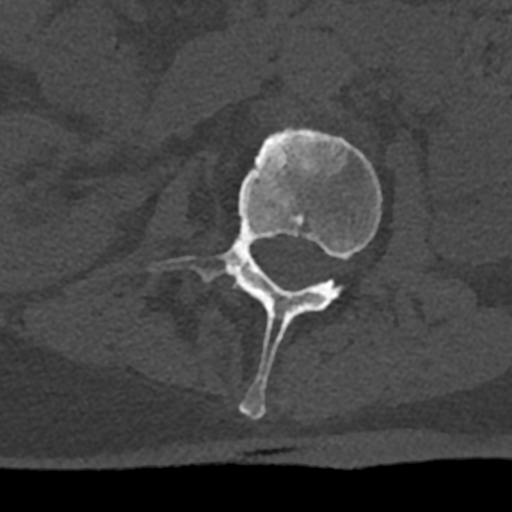
CT including the spine, one axial slice. Slice 373 of 797 in the series (ordered by position). Reconstruction kernel Br40s/3. Bone window (W 1800 / L 400 HU). 512 × 512 image matrix, field of view 160 × 160 mm. Patient: male, 74 years. Case-level facts recorded for this patient, not image findings: primary cancer: renal.
Outlined on this slice (semi-automatic segmentation, software-assisted and operator-edited):
- L2 vertebra: bounding box <151,127,382,419> (left, top, right, bottom; pixels)
- L3 vertebra: <234,284,243,290>